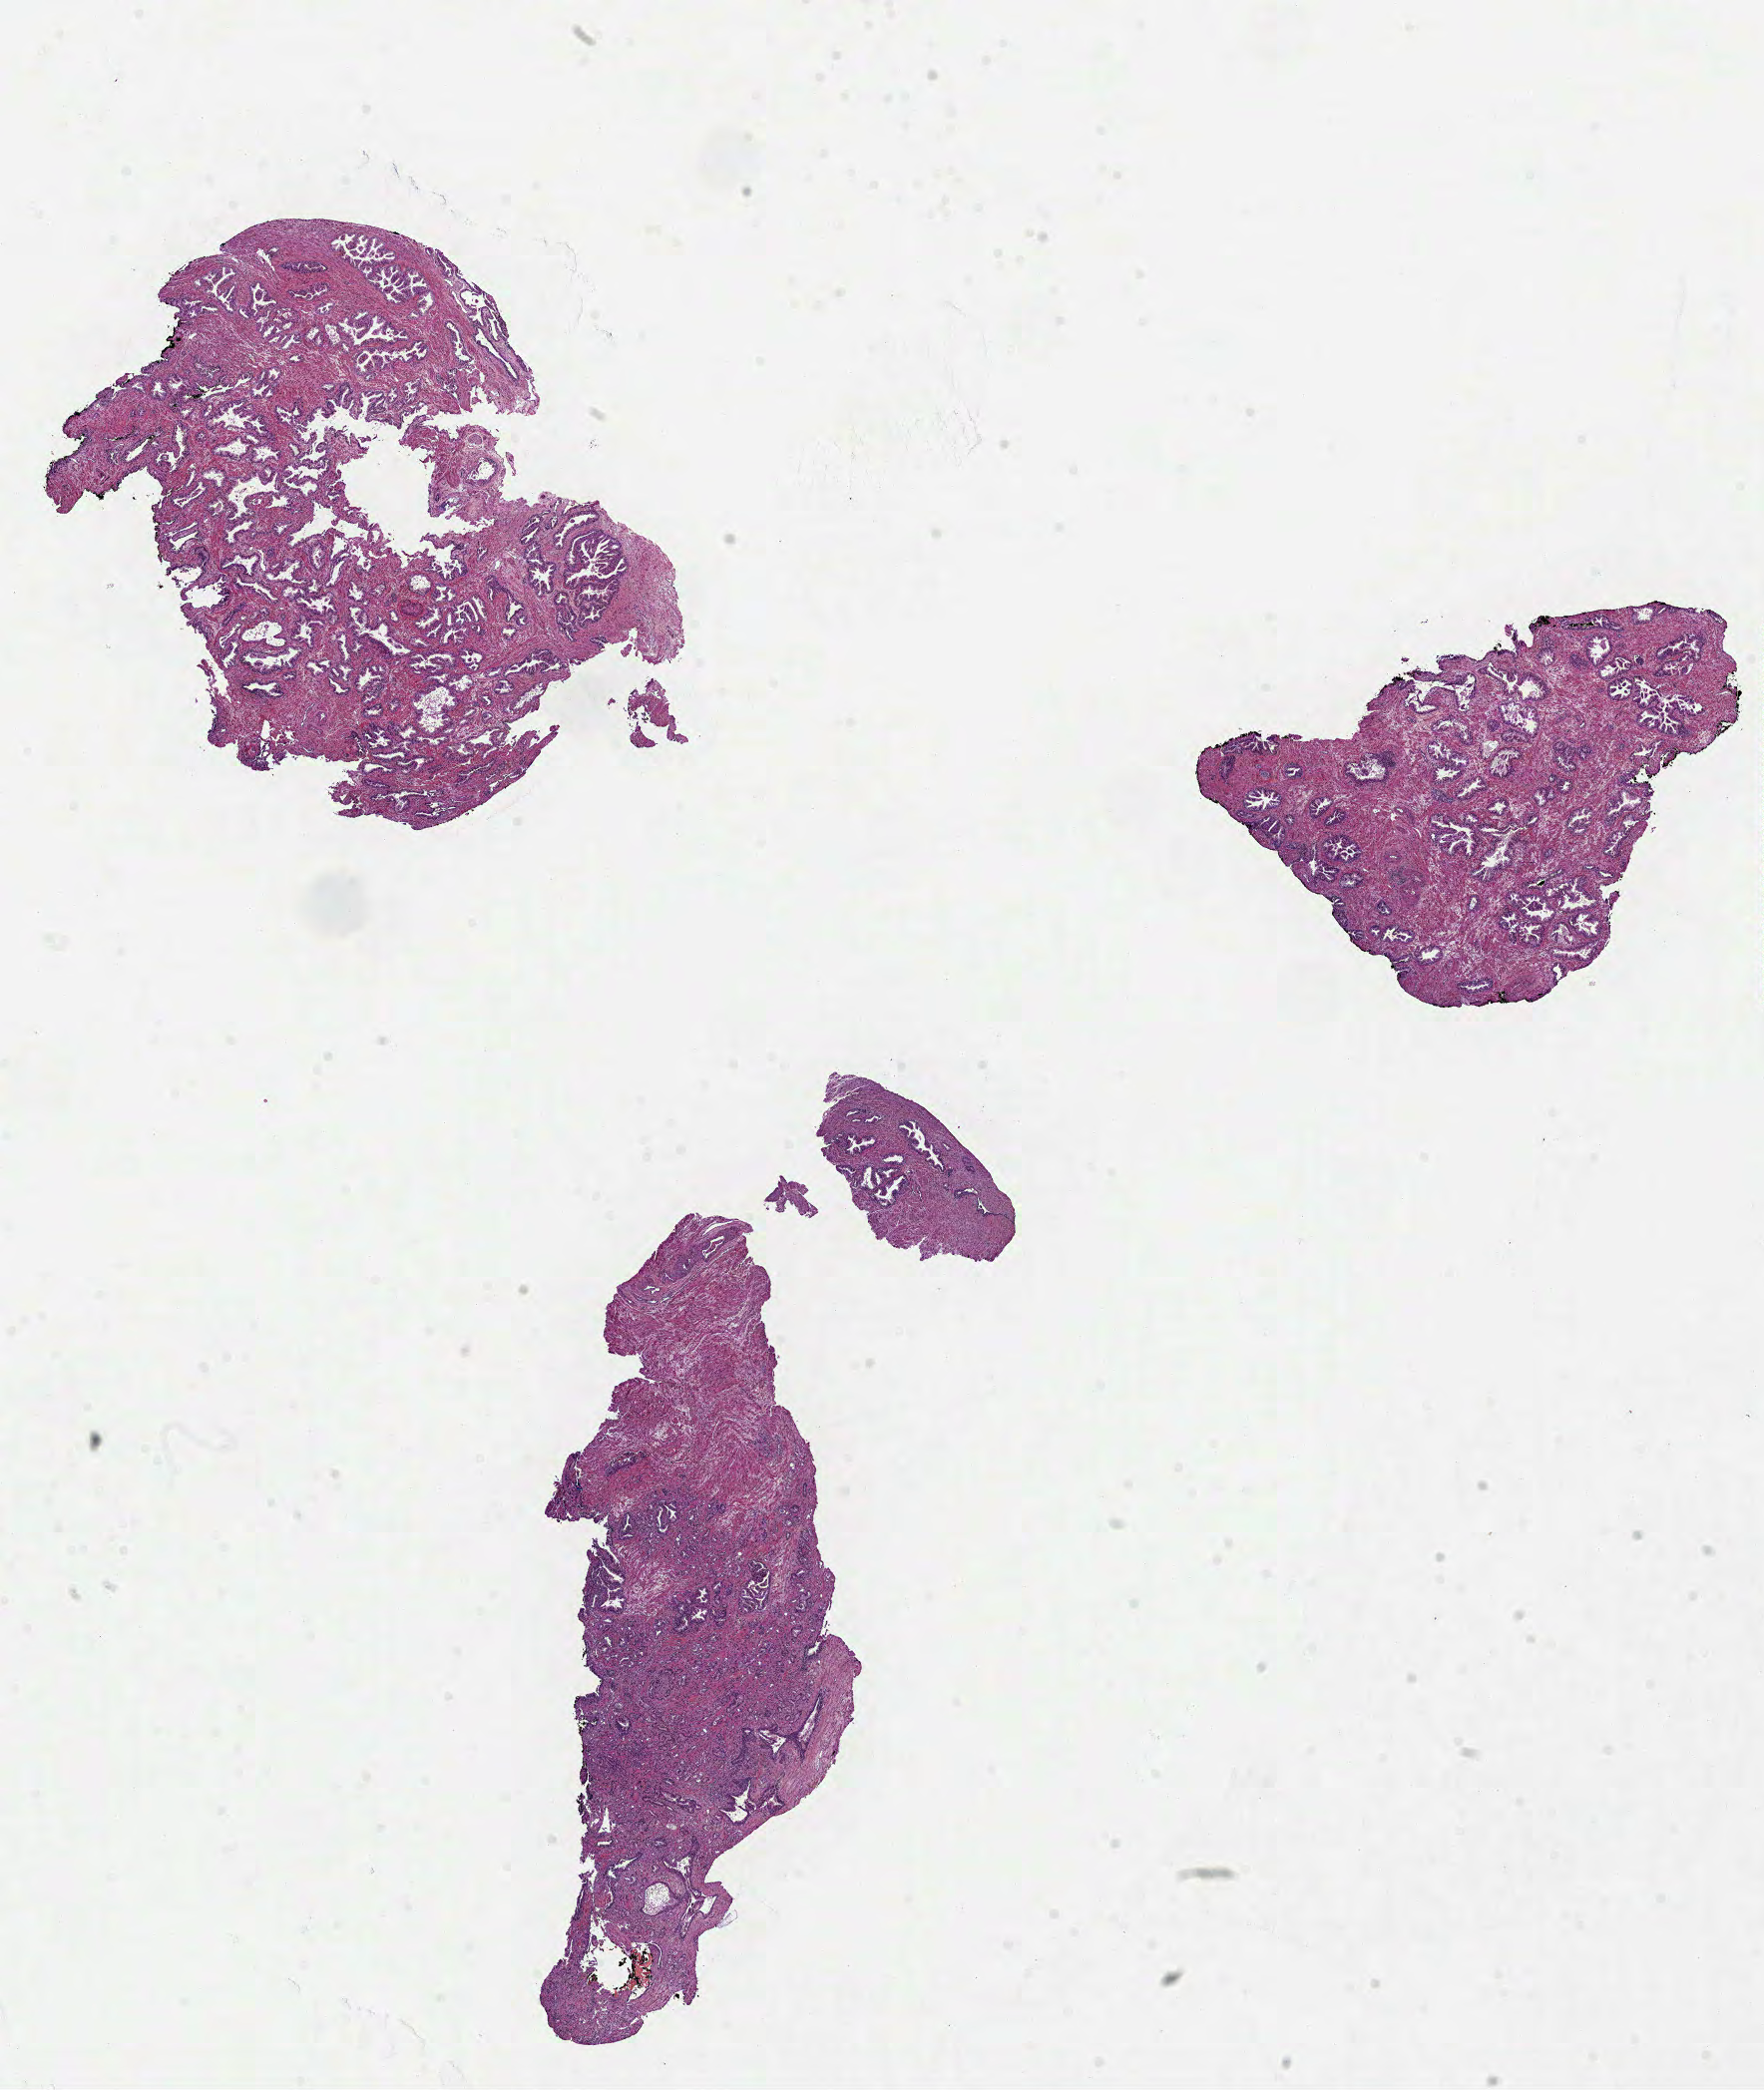
Digitized H&E-stained tissue section (whole slide), low-resolution overview of the scanned area, about 14.3 x 16.9 mm. Formalin-fixed paraffin-embedded (FFPE) diagnostic section. Sample: primary tumour, prostate. Male, age 65 years at initial diagnosis. Gleason score: 7 (4+3).
Laterality: bilateral. Lymph nodes positive (case pathology): 0 of 3 examined. Pathologic diagnosis: Acinar cell carcinoma.